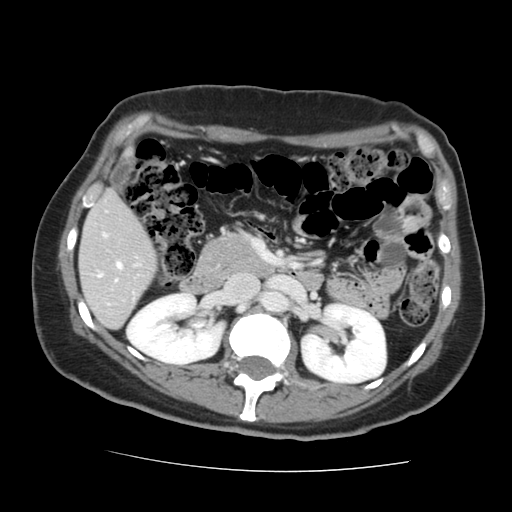
Contrast-enhanced abdominal CT, one axial slice. Slice 68 of 144 in the series (ordered by position). Intravenous contrast given. Soft-tissue window (W 400 / L 40 HU). 2.5 mm slice thickness. 512 × 512 image matrix, field of view 333 × 333 mm. Female patient, age 46 years. From the clinical record (not read from this slice): diagnosis: colorectal cancer liver metastases, imaged before liver resection; multiple liver metastases: no; largest metastasis: 2.8 cm.
Structures marked on this image (manually delineated by an expert):
- liver: bounding box [x1, y1, x2, y2] px = [80, 193, 156, 328]
- planned liver remnant (the part of the liver to remain after resection): [80, 193, 156, 321]
- portal vein (with intrahepatic branches): [98, 234, 122, 282]